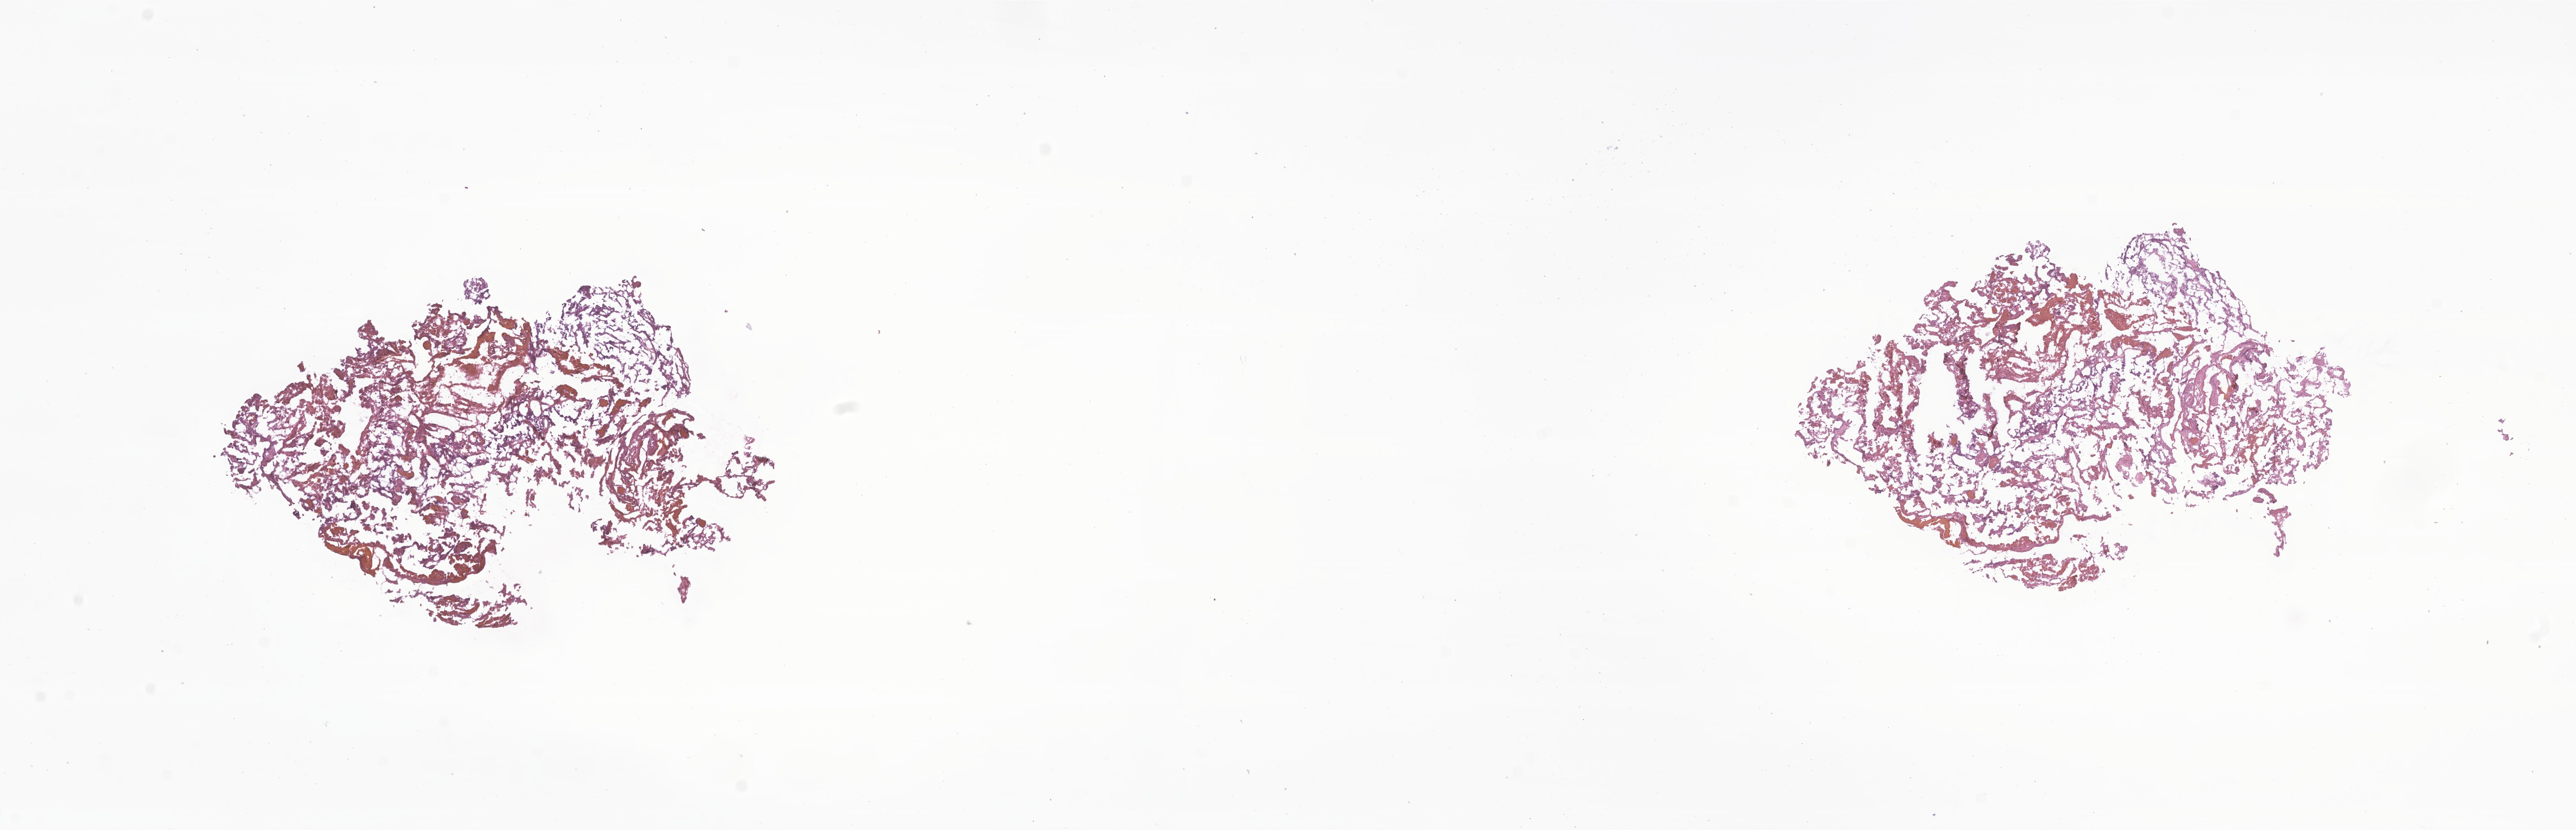
Whole-slide image, hematoxylin and eosin (H&E) stain of tumor tissue from the brain — low-resolution overview of the scanned area, about 22.2 x 7.1 mm, frozen section. Female patient, age 145 months (12 years 1 month).
- diagnosis: Embryonal carcinoma, NOS